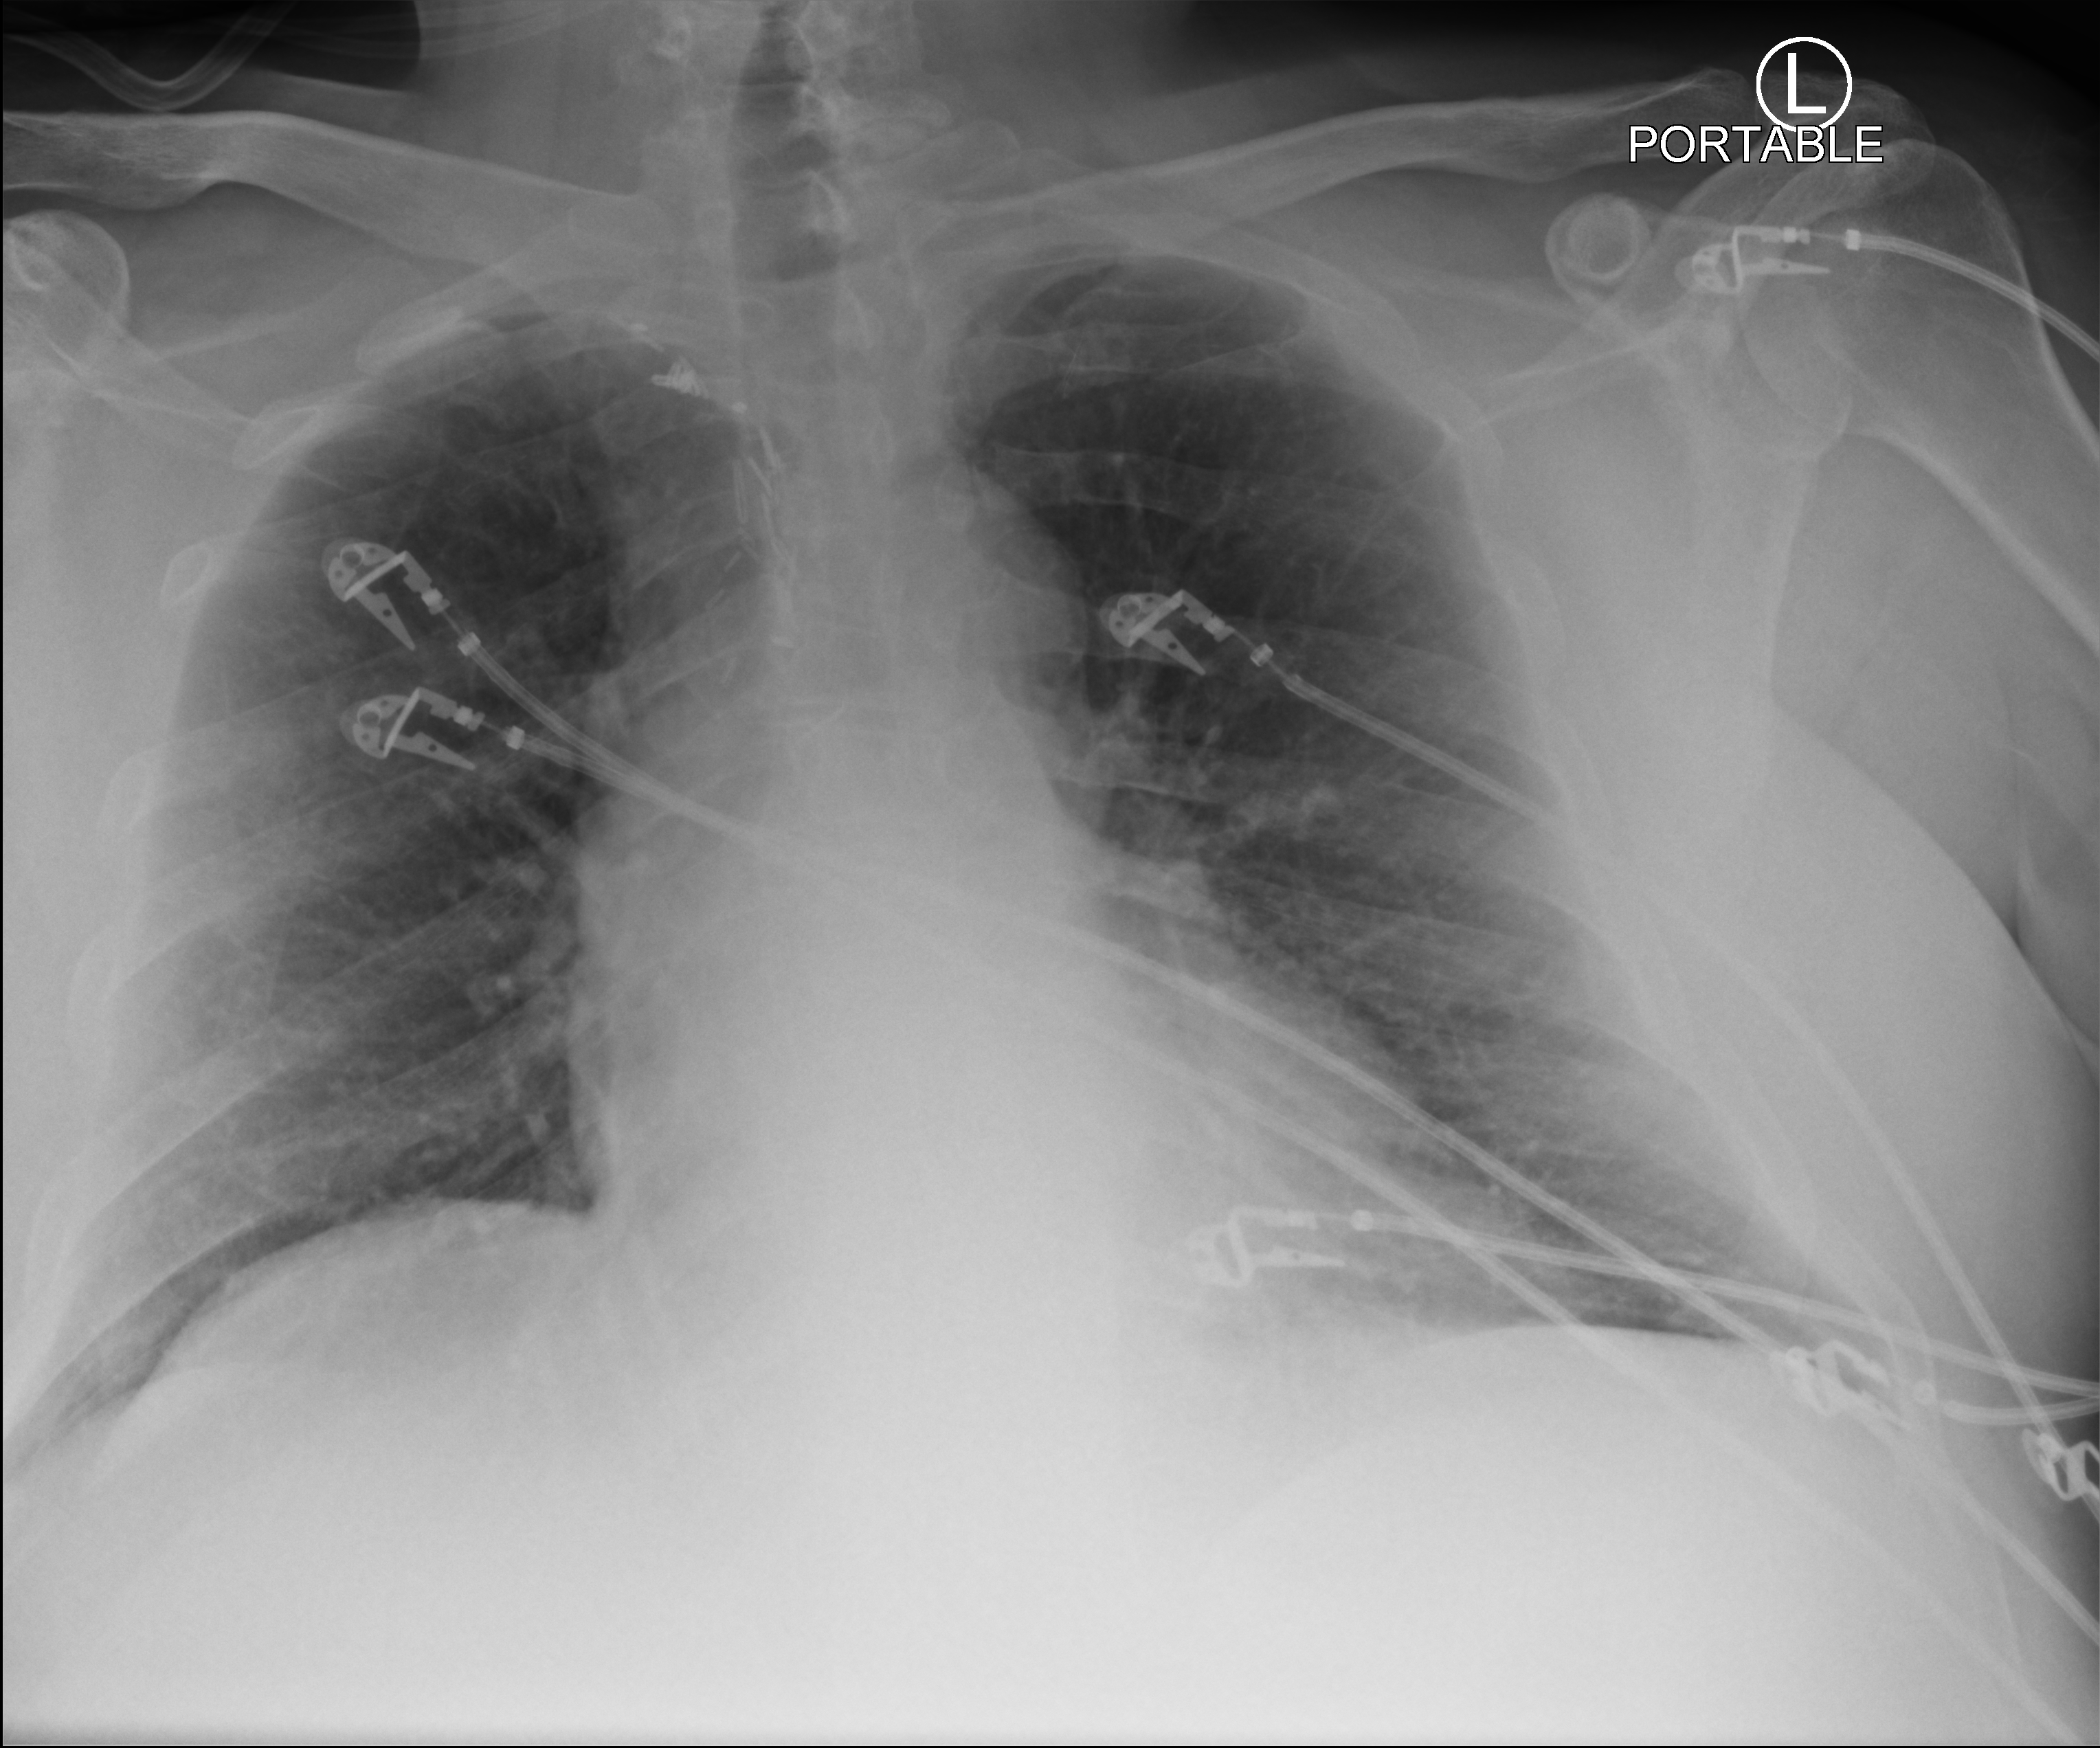
Portable chest radiograph; anteroposterior (AP) projection. Patient hospitalised with COVID-19, aged 18–59 years.
From the hospital-stay record, not from the radiograph (when in the stay this image was taken is not recorded): mechanically ventilated during this hospital stay: yes; admitted to intensive care during this hospital stay: yes.